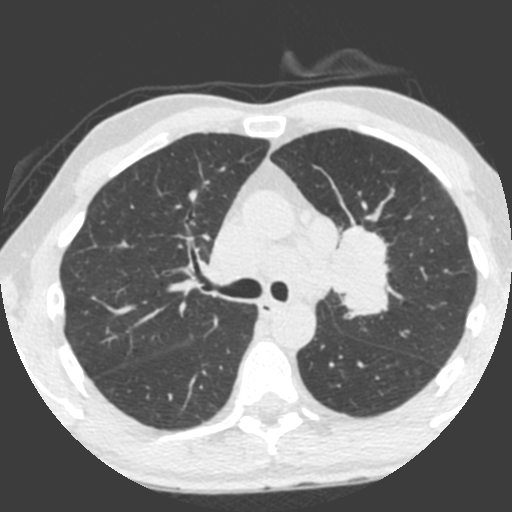
Low-dose screening chest CT, axial slice. Third screening round (two years after baseline). Lung window (W 1500 / L -600 HU). 2 mm slice thickness. Standard (soft-tissue) reconstruction kernel (B). Slice 143 of 212 in the series. 512 × 512 image matrix. Male participant, aged 55 years at enrolment. Current smoker at enrolment.
Lesion marked by an expert reader, bounding box (x1, y1, x2, y2) in pixels: (309, 225, 394, 324). Reader record for this screening exam (exam-level; its link to the box is not recorded): non-calcified nodule or mass ≥4 mm, left upper lobe, 49 × 29 mm, spiculated (stellate) margins, soft tissue attenuation, pre-existing on the prior screen: yes; interval growth: yes. Official screen result: positive, other. Later outcome: lung cancer diagnosed 0 days after this screen — small cell carcinoma, NOS, left upper lobe, undifferentiated (G4), stage IV (AJCC 6th edition), 60 mm at pathology.